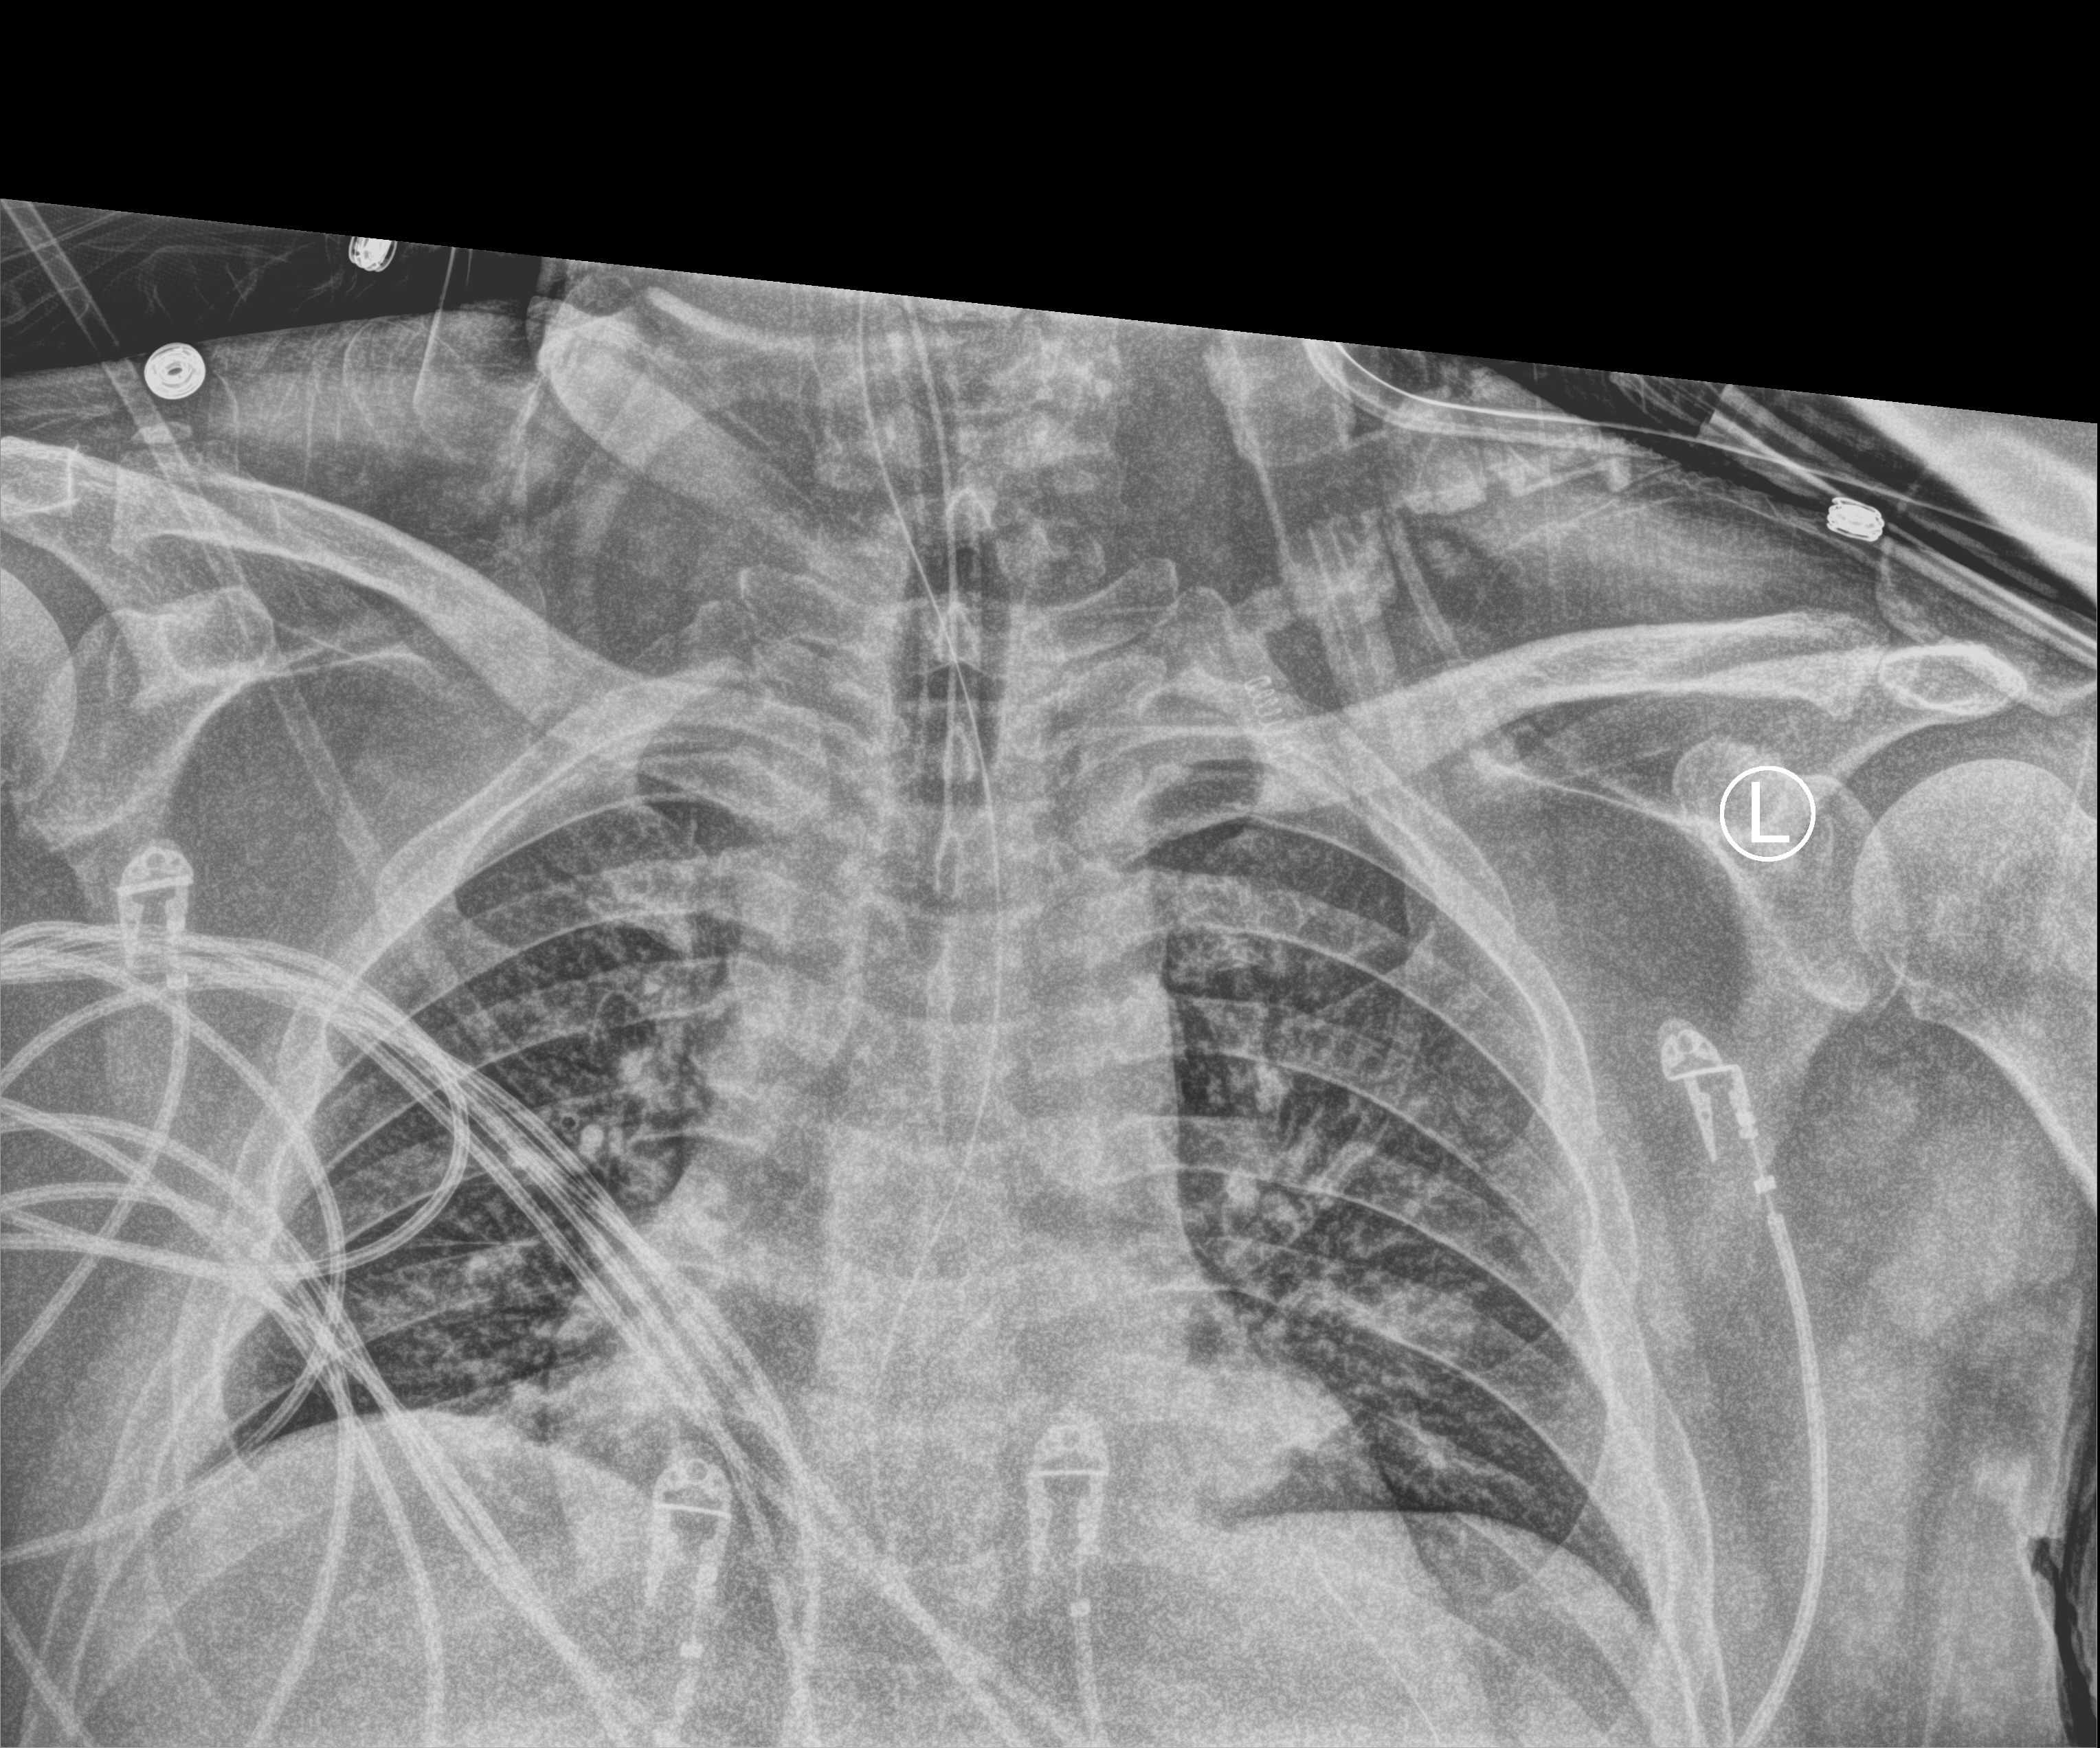
Portable chest radiograph, anteroposterior (AP) projection. Patient hospitalised with COVID-19; male, aged 18–59 years.
Admission-level facts for this patient (not findings on this image; timing relative to this image not recorded):
- mechanically ventilated during this hospital stay: yes